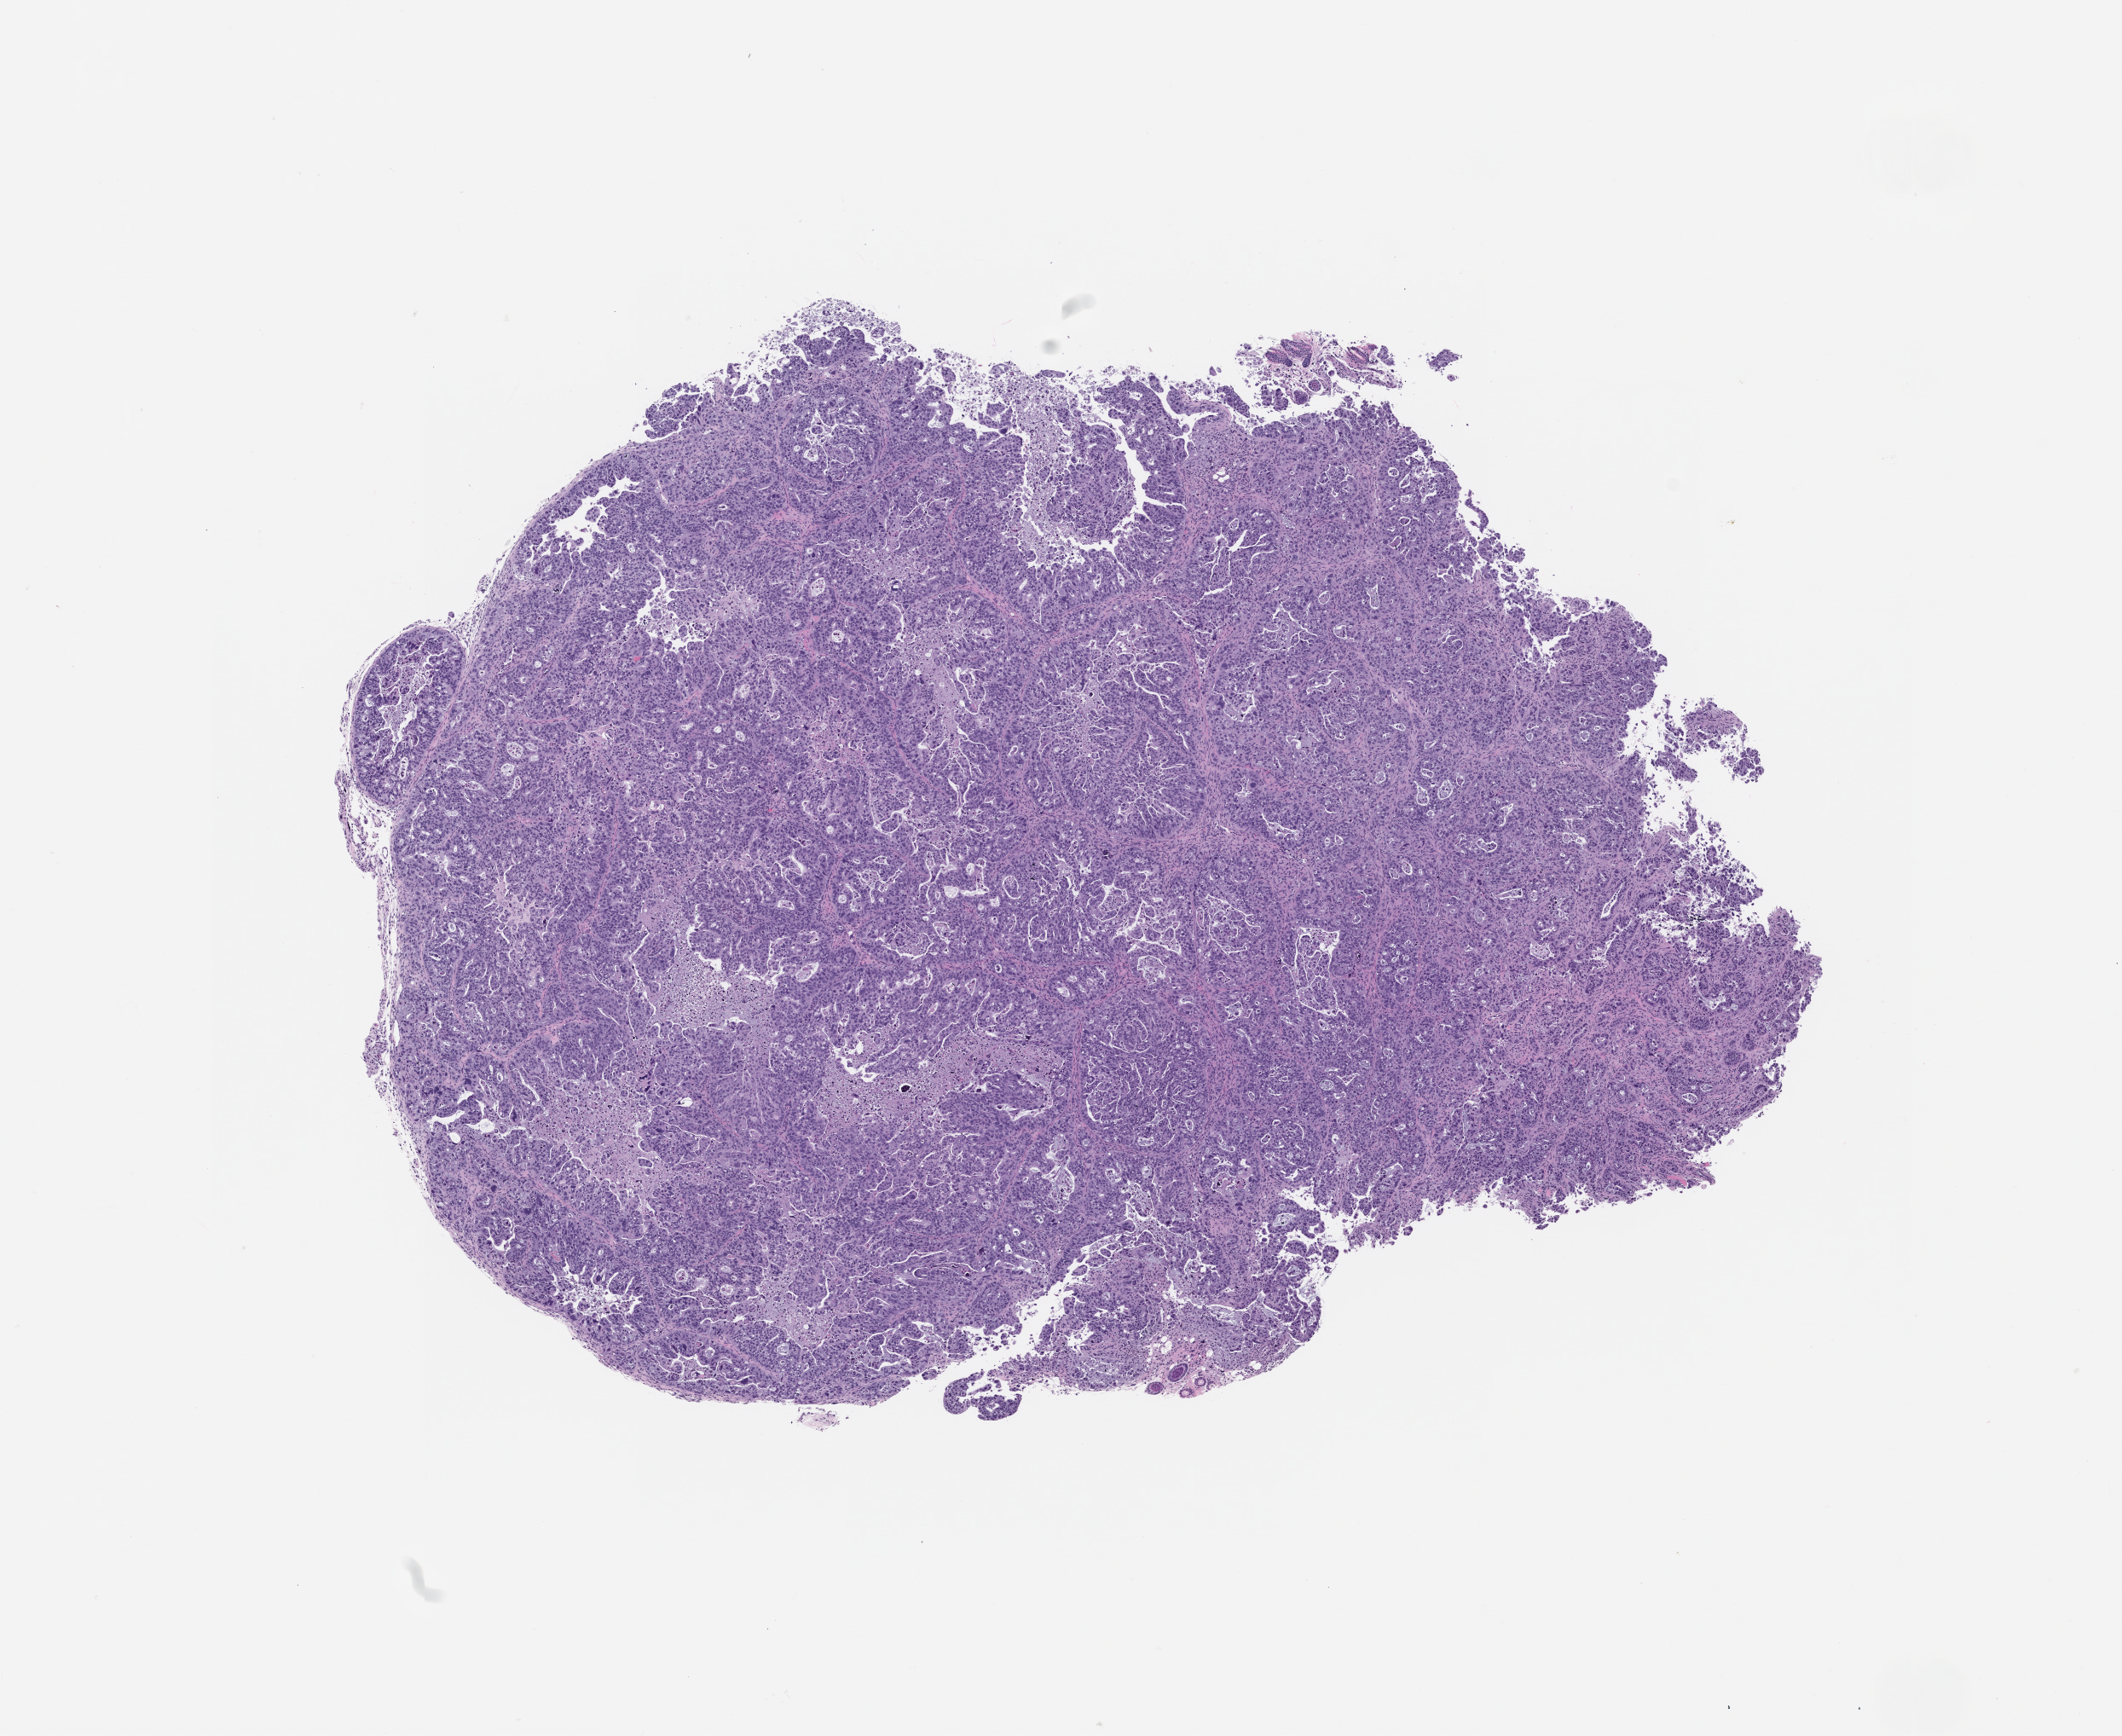
Hematoxylin and eosin (H&E) whole-slide image of a patient-derived xenograft (PDX) tumor grown in a mouse, passage 0 — a low-resolution overview of the entire scanned area, about 10.0 x 8.2 mm; FFPE section; originating tumor site category: pancreas.
Originating patient diagnosis: Pancreatic Adenocarcinoma.